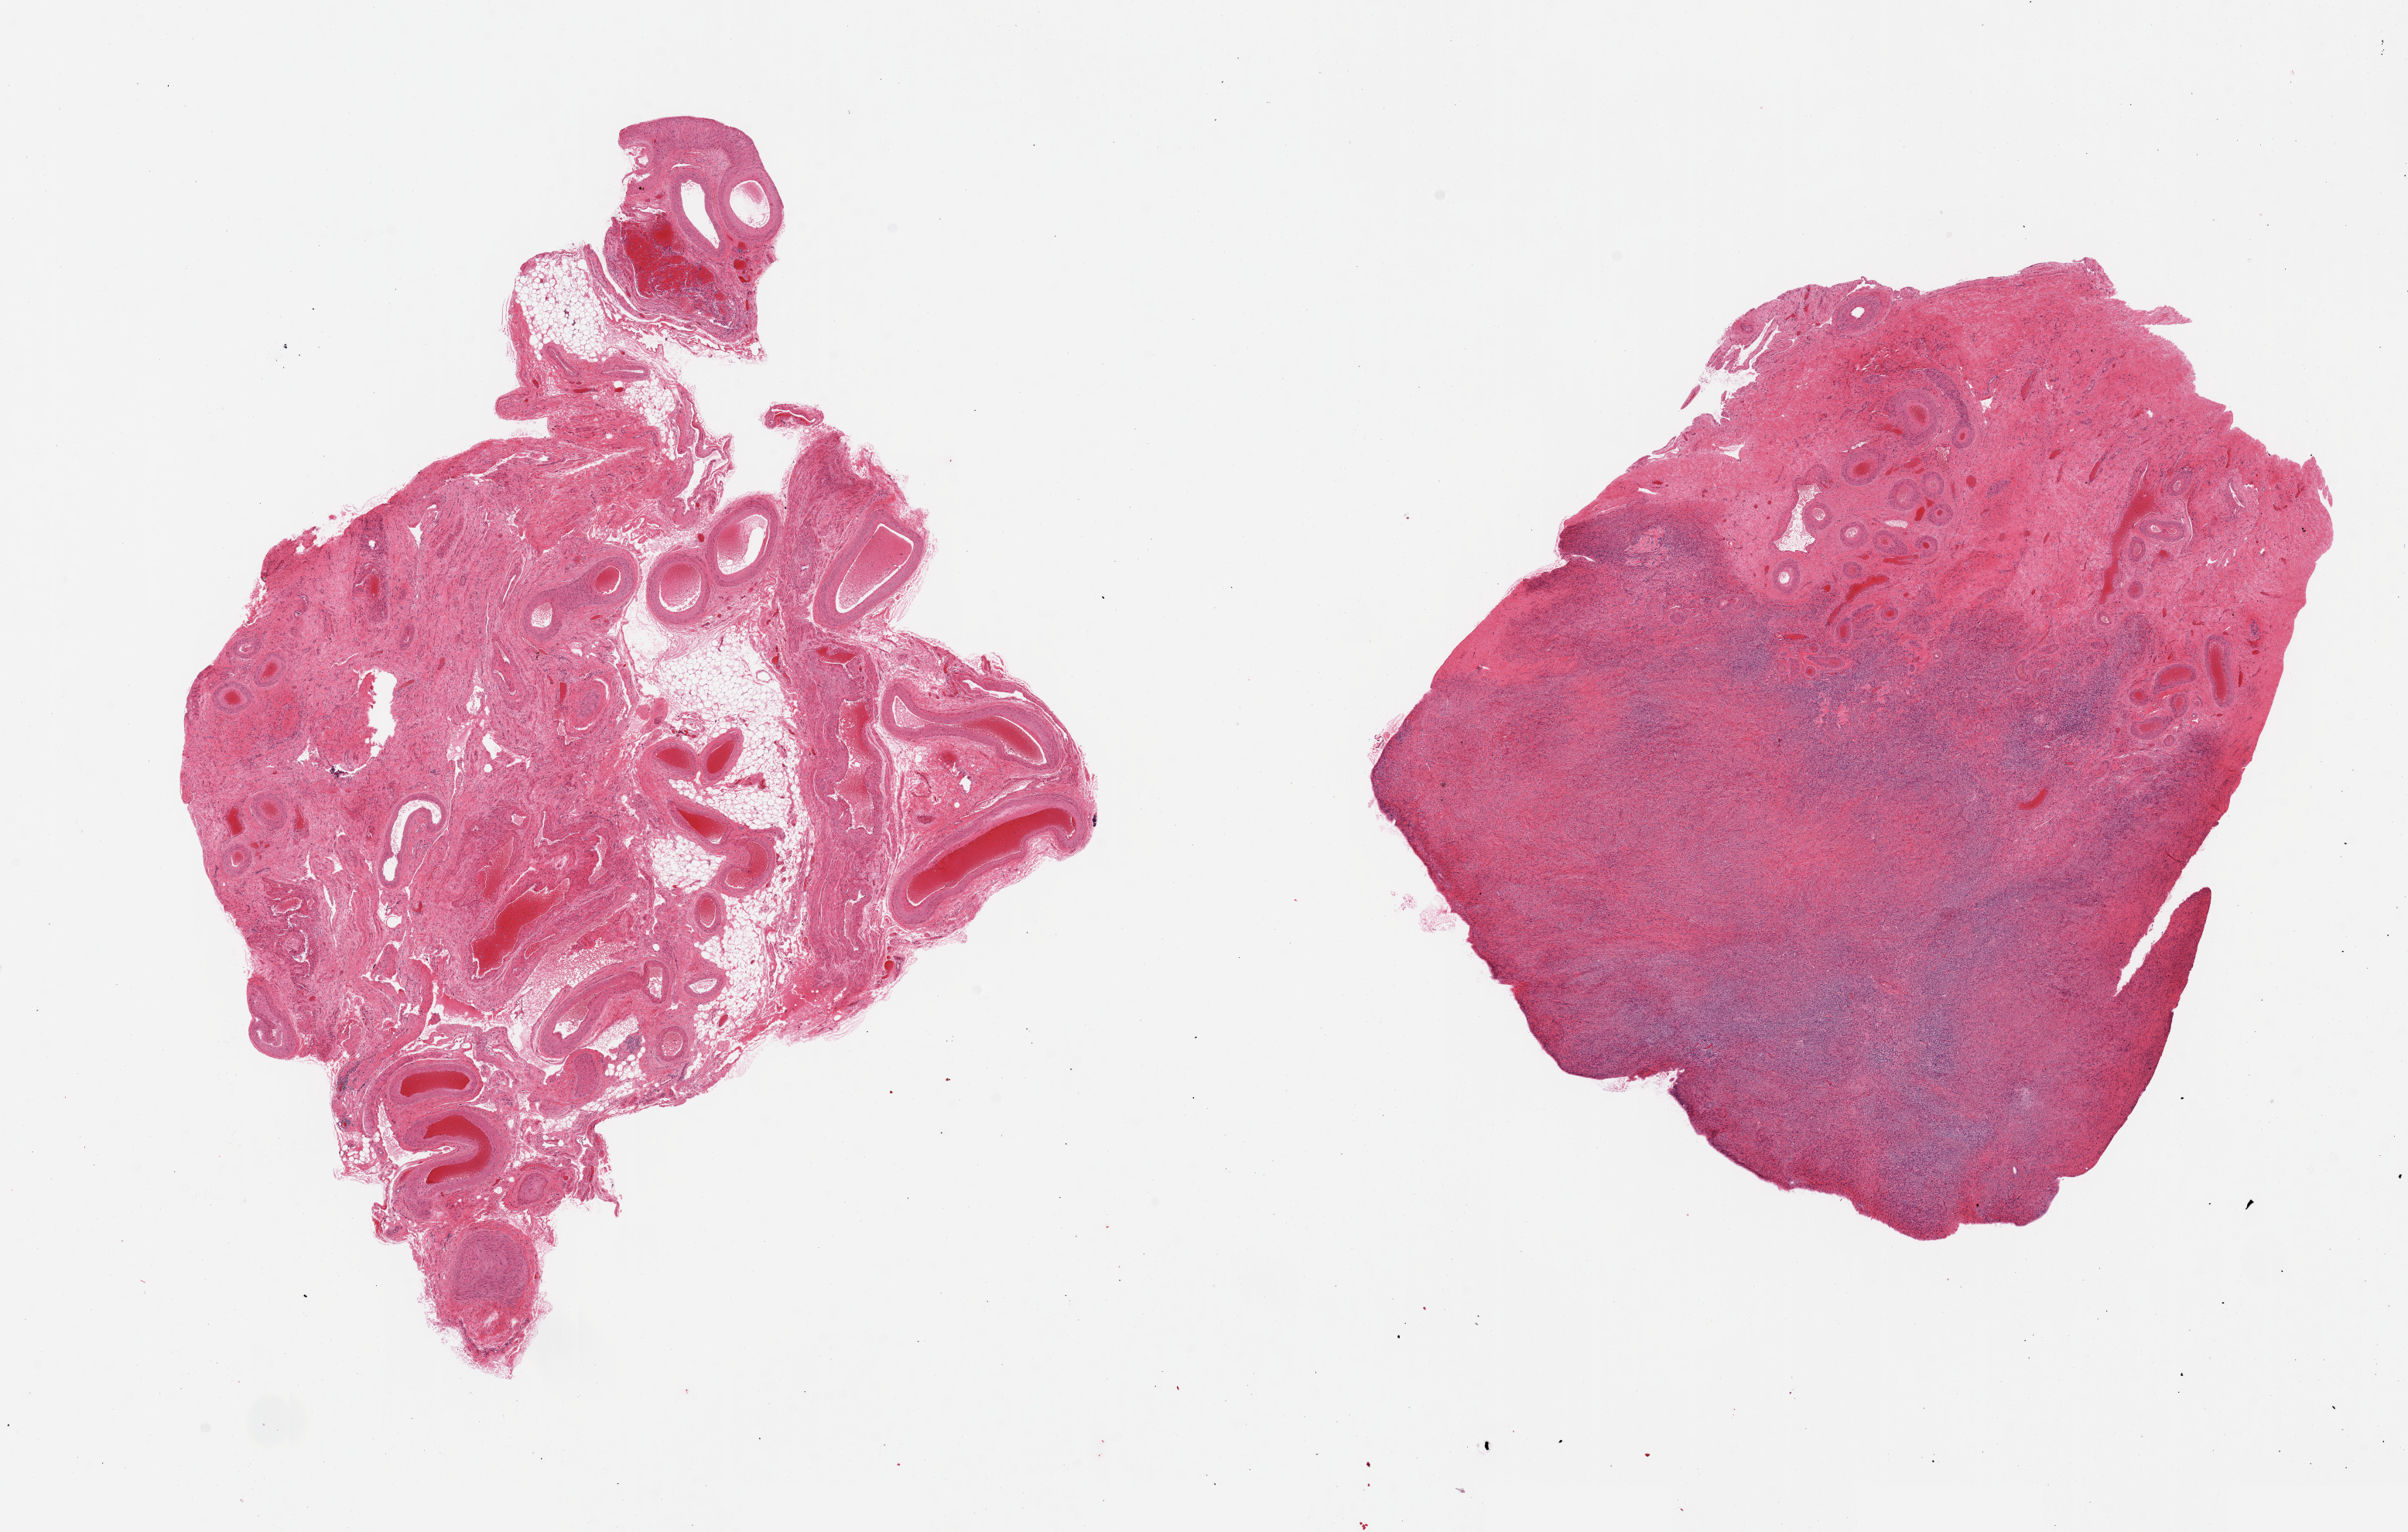
Whole-slide image, hematoxylin and eosin (H&E) stain — shown as a low-resolution overview of the whole scanned area (about 24.6 x 15.7 mm), PAXgene-fixed paraffin-embedded (PFPE) section, target tissue: ovary, tissue donor sample. Donor sex: female.
* reviewer comment on this tissue sample: 2 pieces: 1 atrophic with 30% fibrosis; other piece is all fibrovascular and adipose, no ovary